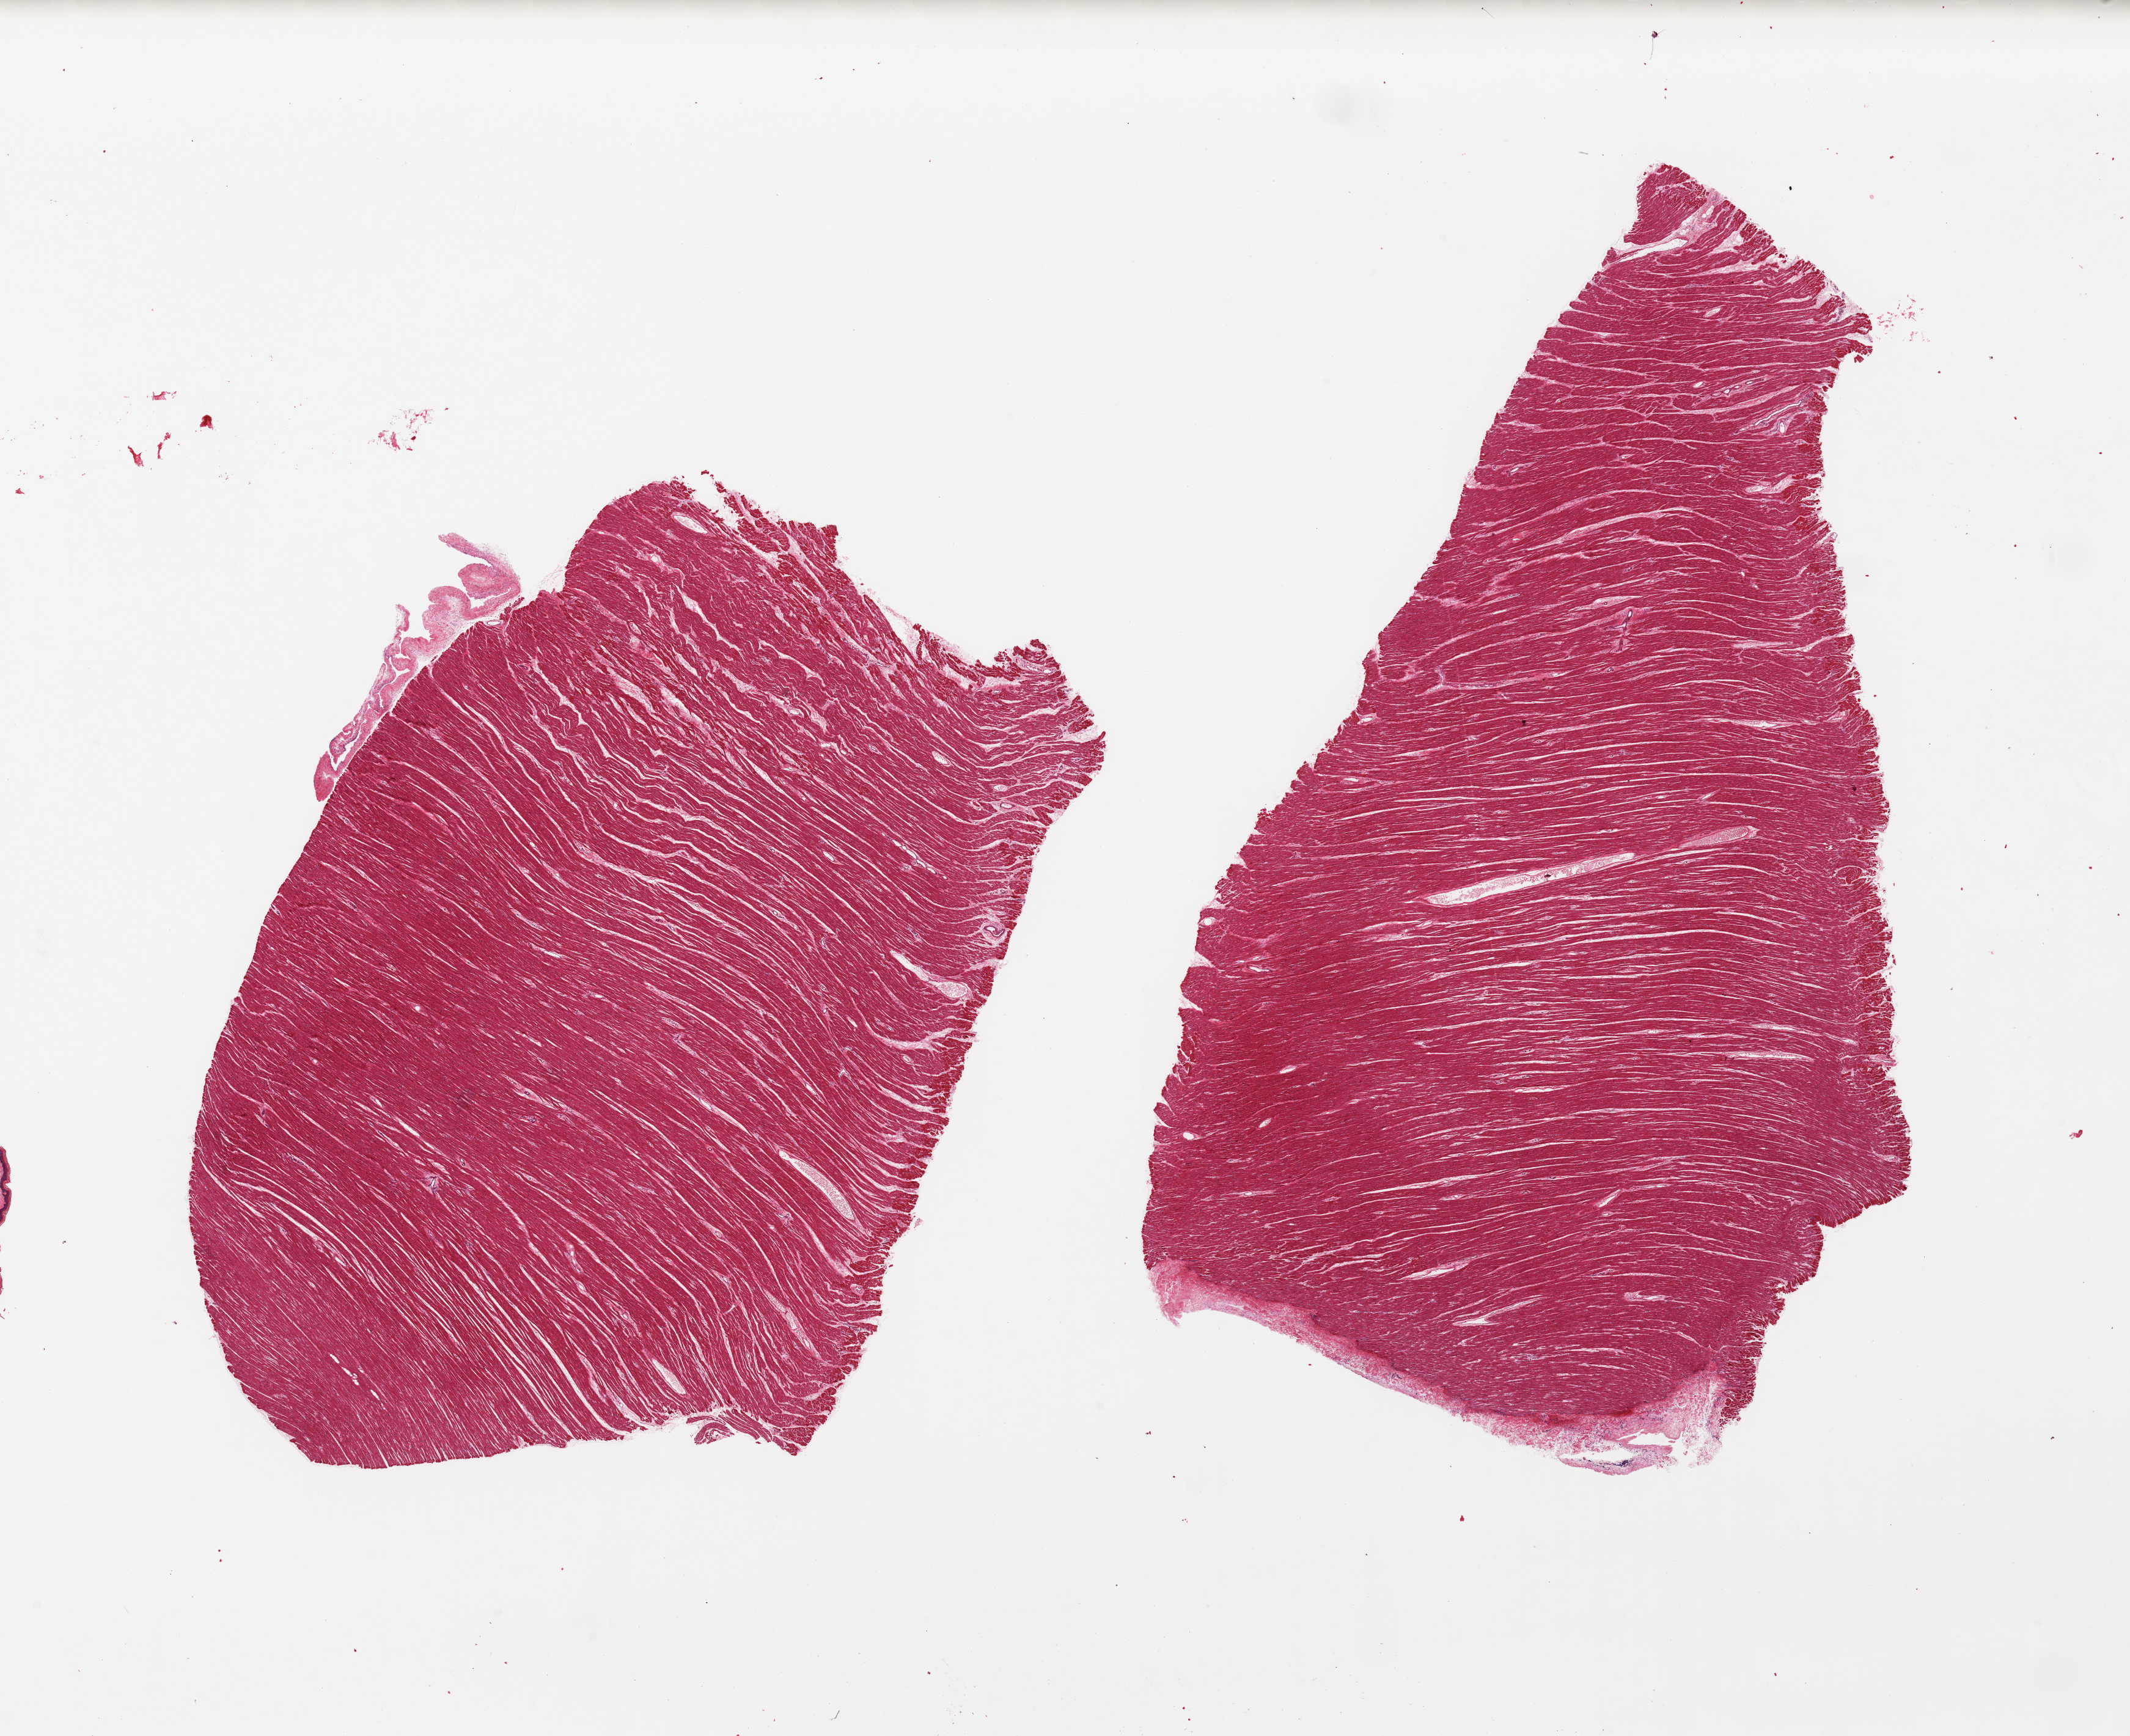
Haematoxylin and eosin whole-slide image, brightfield, shown as a low-resolution overview of the whole scanned area (about 27.6 x 22.5 mm, acquisition: 20x scan); PAXgene-fixed paraffin-embedded (PFPE) section; section of heart (target tissue); tissue donor sample. Donor sex: male.
* reviewer comment on this tissue sample: 2 pieces, no ischemic changes